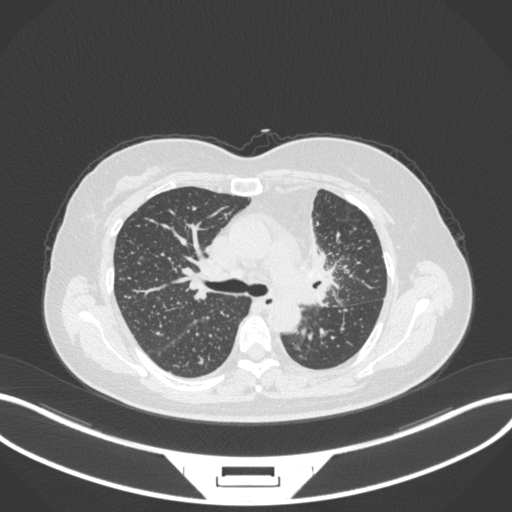
Chest CT, one axial slice. 120 kVp. Lung window (W 1500 / L -600 HU). 1 mm slice thickness. 512 × 512 image matrix, field of view 400 × 400 mm. Female patient, age 49 years. Case-level facts recorded for this patient, not image findings: clinical TNM (as recorded): T1c N0 M1.
Annotated regions visible in this slice (bounding box drawn by a radiologist):
- lung tumour (recorded histology: adenocarcinoma): bounding box (x1, y1, x2, y2) in pixels: (292, 215, 344, 307)